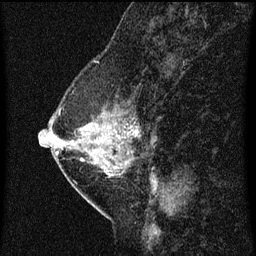
Breast MRI (dynamic contrast-enhanced), one sagittal slice; position 23 of 60 along the scan axis; dynamic contrast-enhanced series, image 2 of 3 at this slice position (ordered by acquisition); 1.5 T; TE 4.2 ms, TR 8 ms; 2 mm slice thickness; 256 × 256 image matrix. Patient: female, 47 years.
Structures marked on this image (semi-automatically segmented with operator editing):
- analysis volume of interest (the breast-tissue region the enhancement analysis was run in; not a lesion): bounding box <54,84,141,187> (left, top, right, bottom; pixels)
- tumour enhancement mask (voxels above the 70 % enhancement threshold inside the analysis volume of interest): <58,130,135,163>